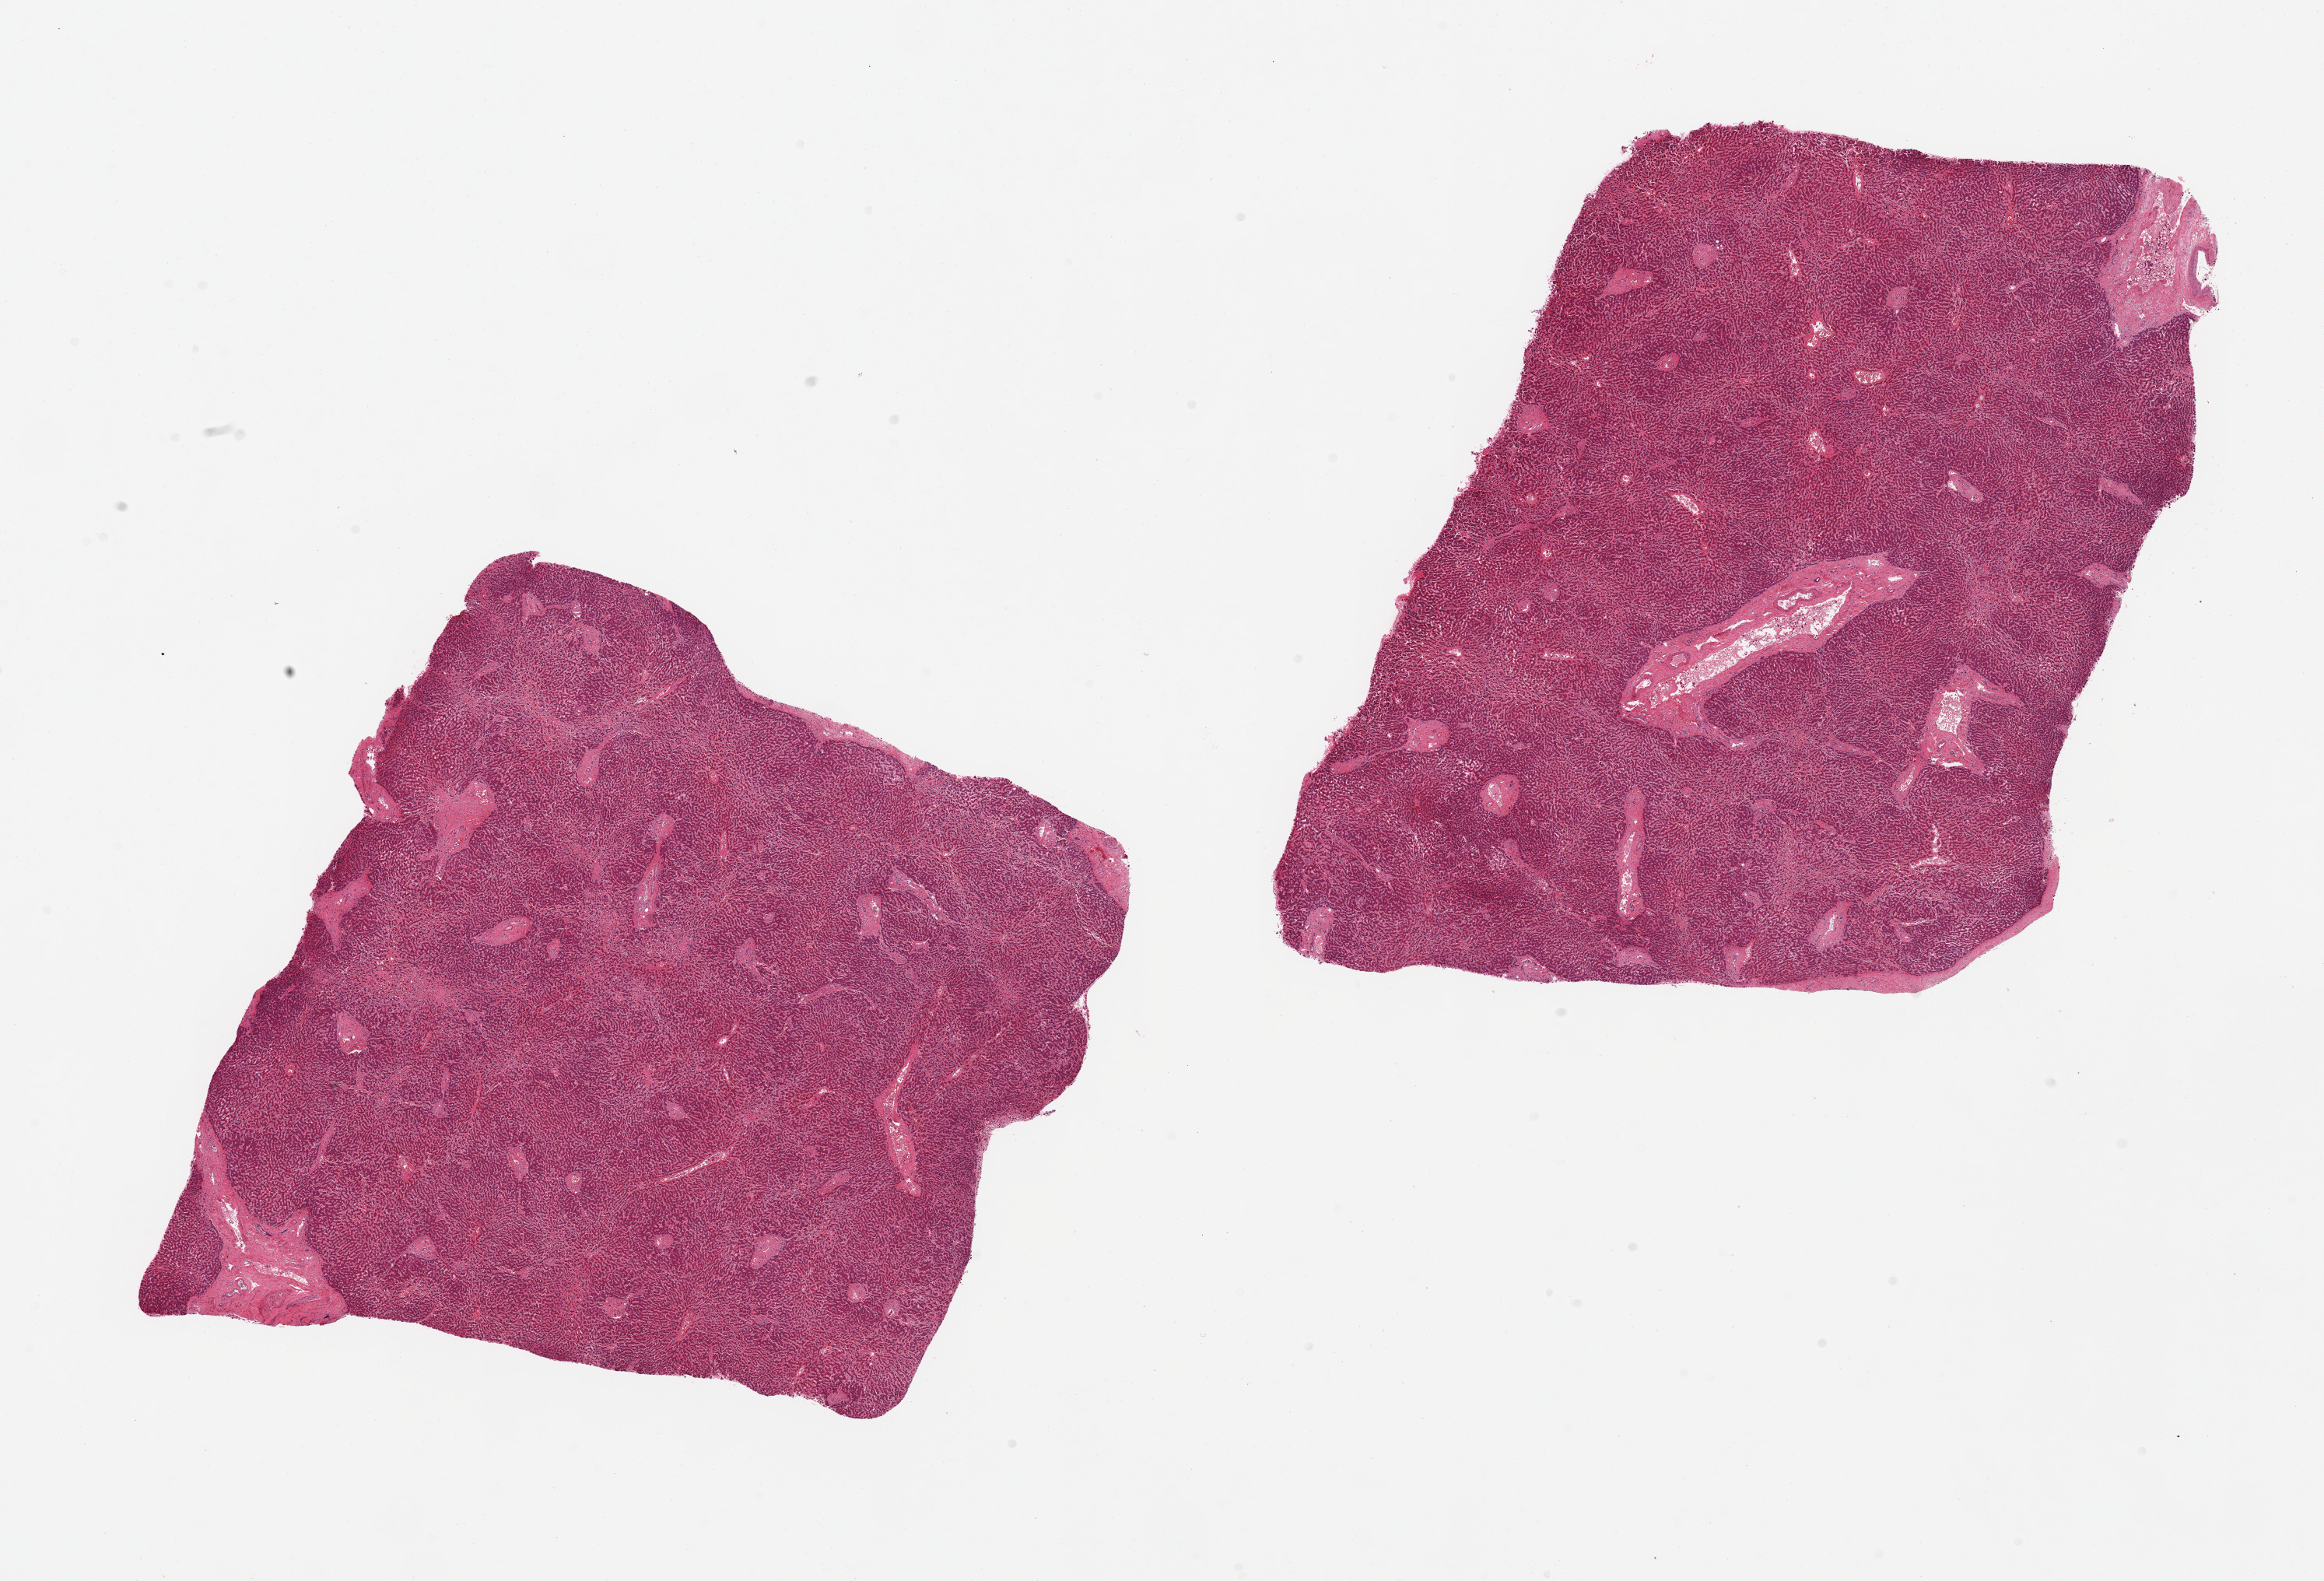
Whole-slide image, haematoxylin and eosin stain — low-resolution overview of the scanned area, about 23.6 x 16.1 mm (acquisition: 20x scan); PAXgene-fixed, paraffin-embedded tissue; target tissue: liver; donor tissue sample. Male donor.
- reviewer comment on this tissue sample: 2 pieces, moderate centrilobular/cardiac congestion, minimal steatosis